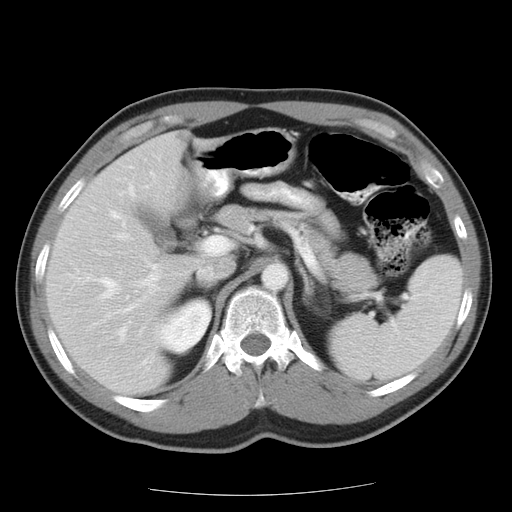
Contrast-enhanced abdominal CT, one axial slice. Slice 11 of 22 in the series (ordered by position). Reconstruction kernel STANDARD. 120 kVp. Intravenous contrast given. Soft-tissue window (W 400 / L 40 HU). 512 × 512 image matrix, field of view 359 × 359 mm. Male patient, age 41 years. Case-level facts recorded for this patient, not image findings: diagnosis: colorectal cancer liver metastases, imaged before liver resection; multiple liver metastases: no; largest metastasis: 2.7 cm; disease in both lobes: no.
Annotated regions visible in this slice (outlined manually by an expert reader):
- hepatic veins: bounding box [x1, y1, x2, y2] px = [104, 213, 126, 341]
- liver: [48, 136, 190, 394]
- planned liver remnant (the part of the liver to remain after resection): [48, 136, 190, 355]
- portal vein (with intrahepatic branches): [142, 266, 159, 287]